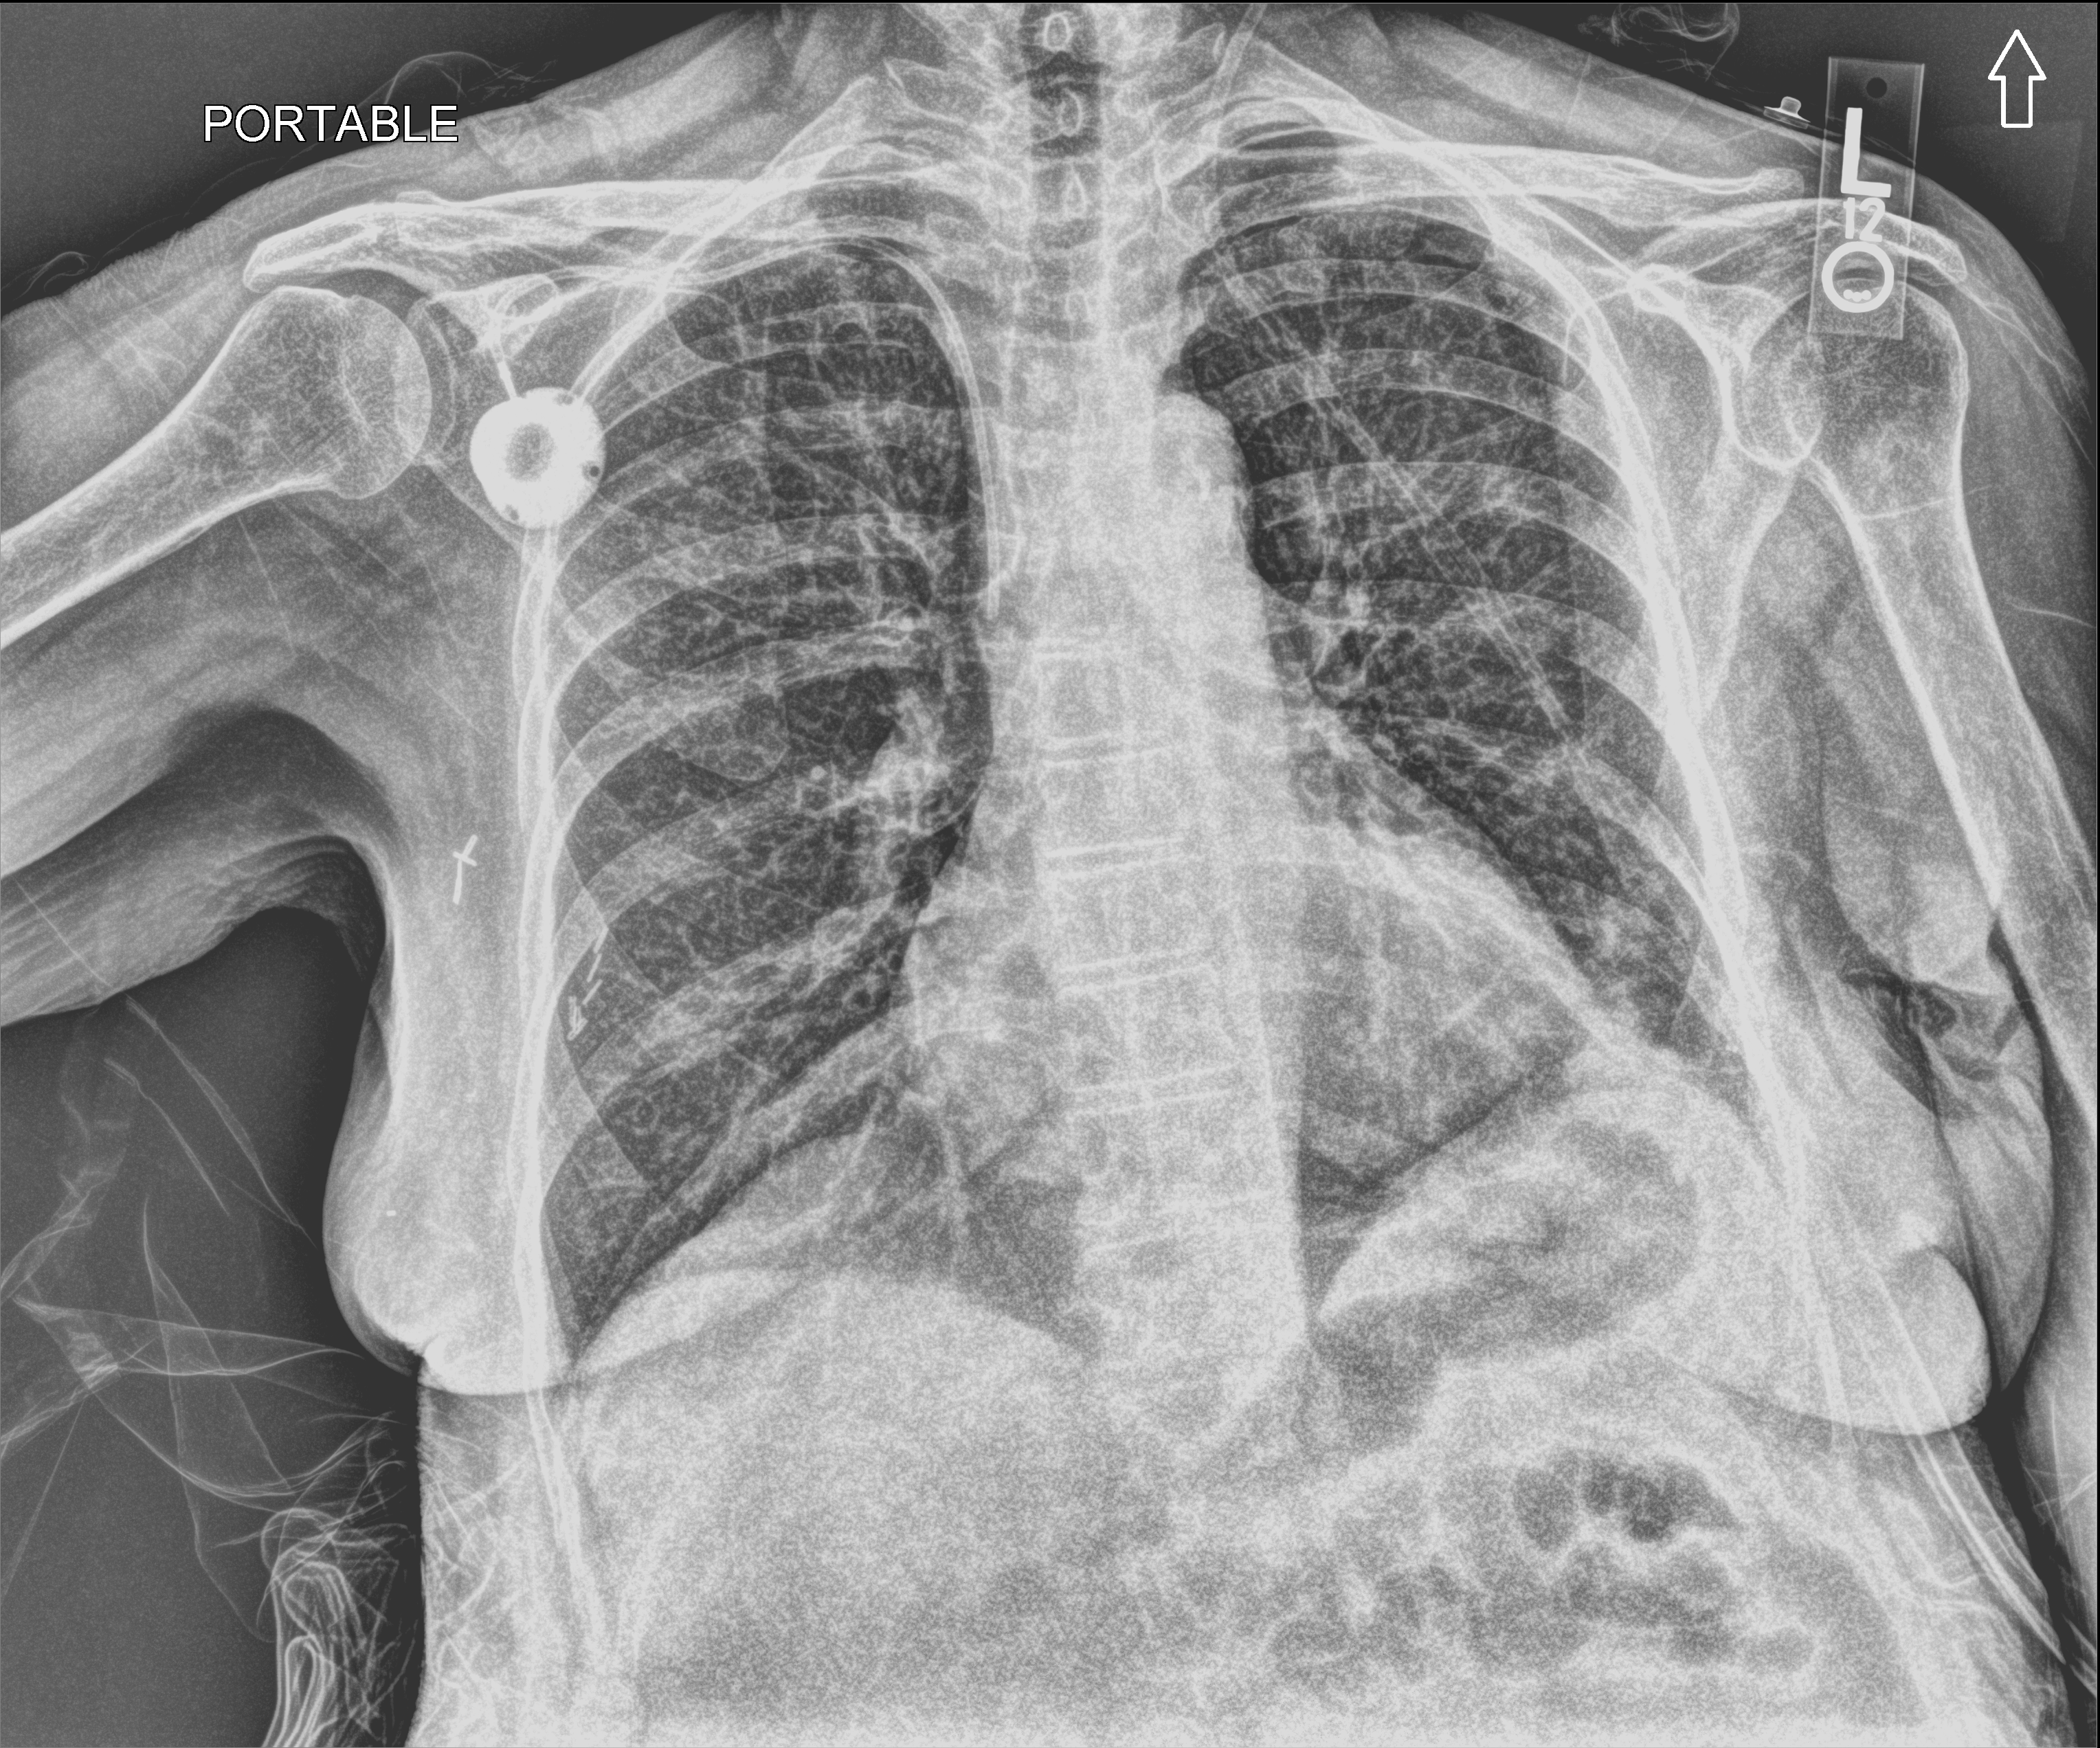
Chest X-ray (portable). Female patient hospitalised with COVID-19, age 60–74 years.
Admission-level facts for this patient (not findings on this image; timing relative to this image not recorded):
- mechanically ventilated during this hospital stay: yes
- length of hospital stay: 43 days